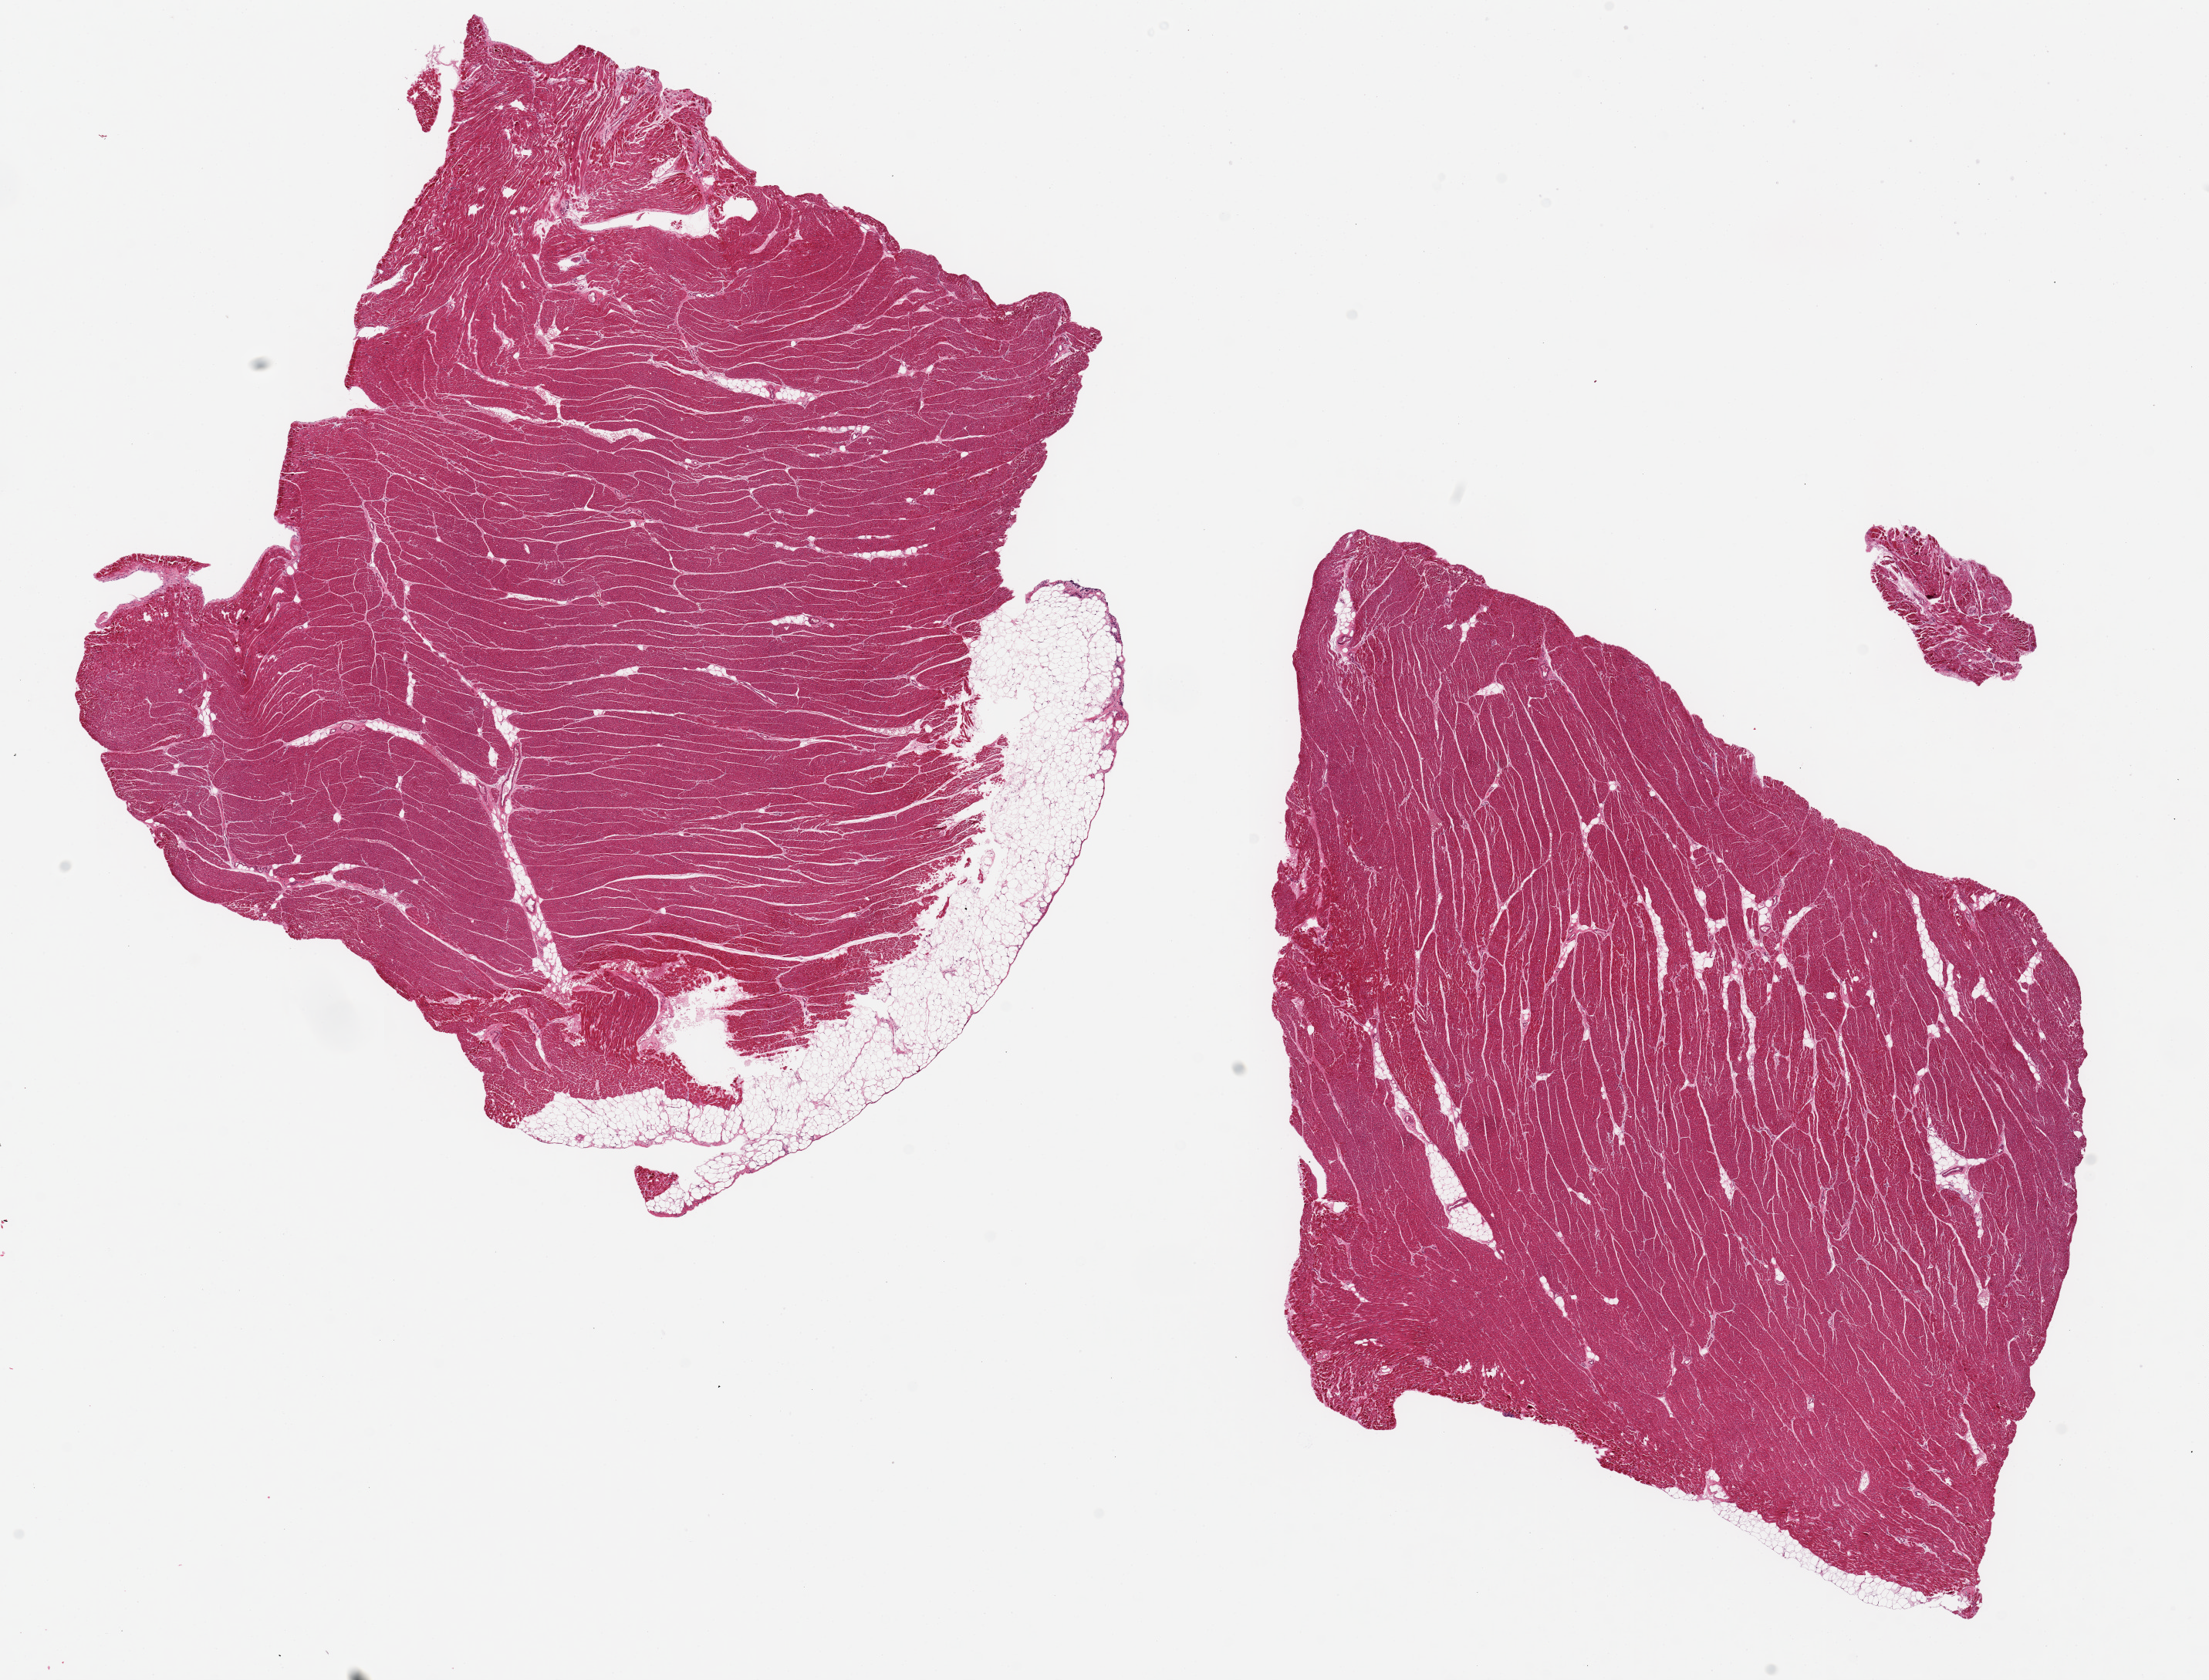
Digitized hematoxylin and eosin (H&E)-stained section — shown as a low-resolution overview of the whole scanned area (about 22.6 x 17.2 mm). PAXgene-fixed paraffin-embedded (PFPE) section. Target tissue: heart. Tissue donor sample. Donor sex: male.
- review note (as recorded): 2 pieces, 11x10 & 10x9mm; Enlarged nuclei c/w hypertension. !x7mm adipose on edge of 1 piece